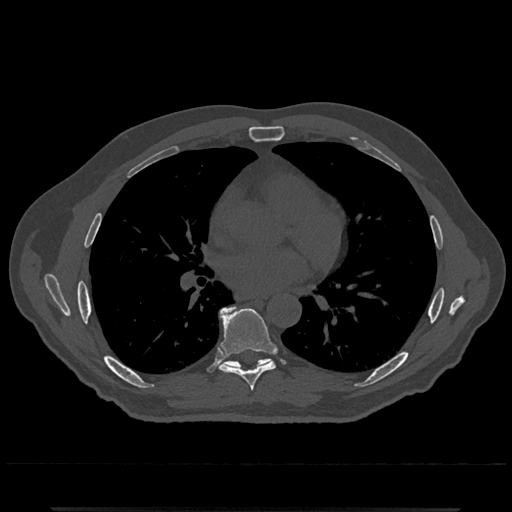
CT including the spine, one axial slice. Slice 708 of 797 in the series (ordered by position). Reconstruction kernel Br40s/3. Bone window (W 1800 / L 400 HU). 0.5 mm slice thickness. 512 × 512 image matrix, field of view 393 × 393 mm. Male patient, age 67 years. Case-level facts recorded for this patient, not image findings: primary cancer: prostate.
Structures marked on this image (semi-automatically segmented with operator editing):
- T7 vertebra: box from (x=218, y=308) to (x=276, y=391) px
- T8 vertebra: (x=219, y=306)–(x=271, y=369)